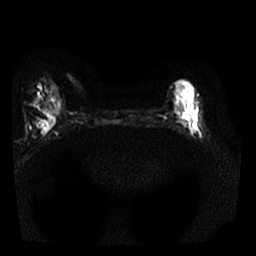
Breast MRI, one axial slice. Position 9 of 25 along the scan axis. Diffusion-weighted series; image 2 of 4 stored at this slice position (different b-values; order by instance number). 1.5 T. 4 mm slice thickness. 256 × 256 image matrix, field of view 300 × 300 mm. Female patient.
Structures marked on this image (expert manual segmentation):
- tumour on diffusion-weighted imaging: box from (x=185, y=110) to (x=202, y=138) px